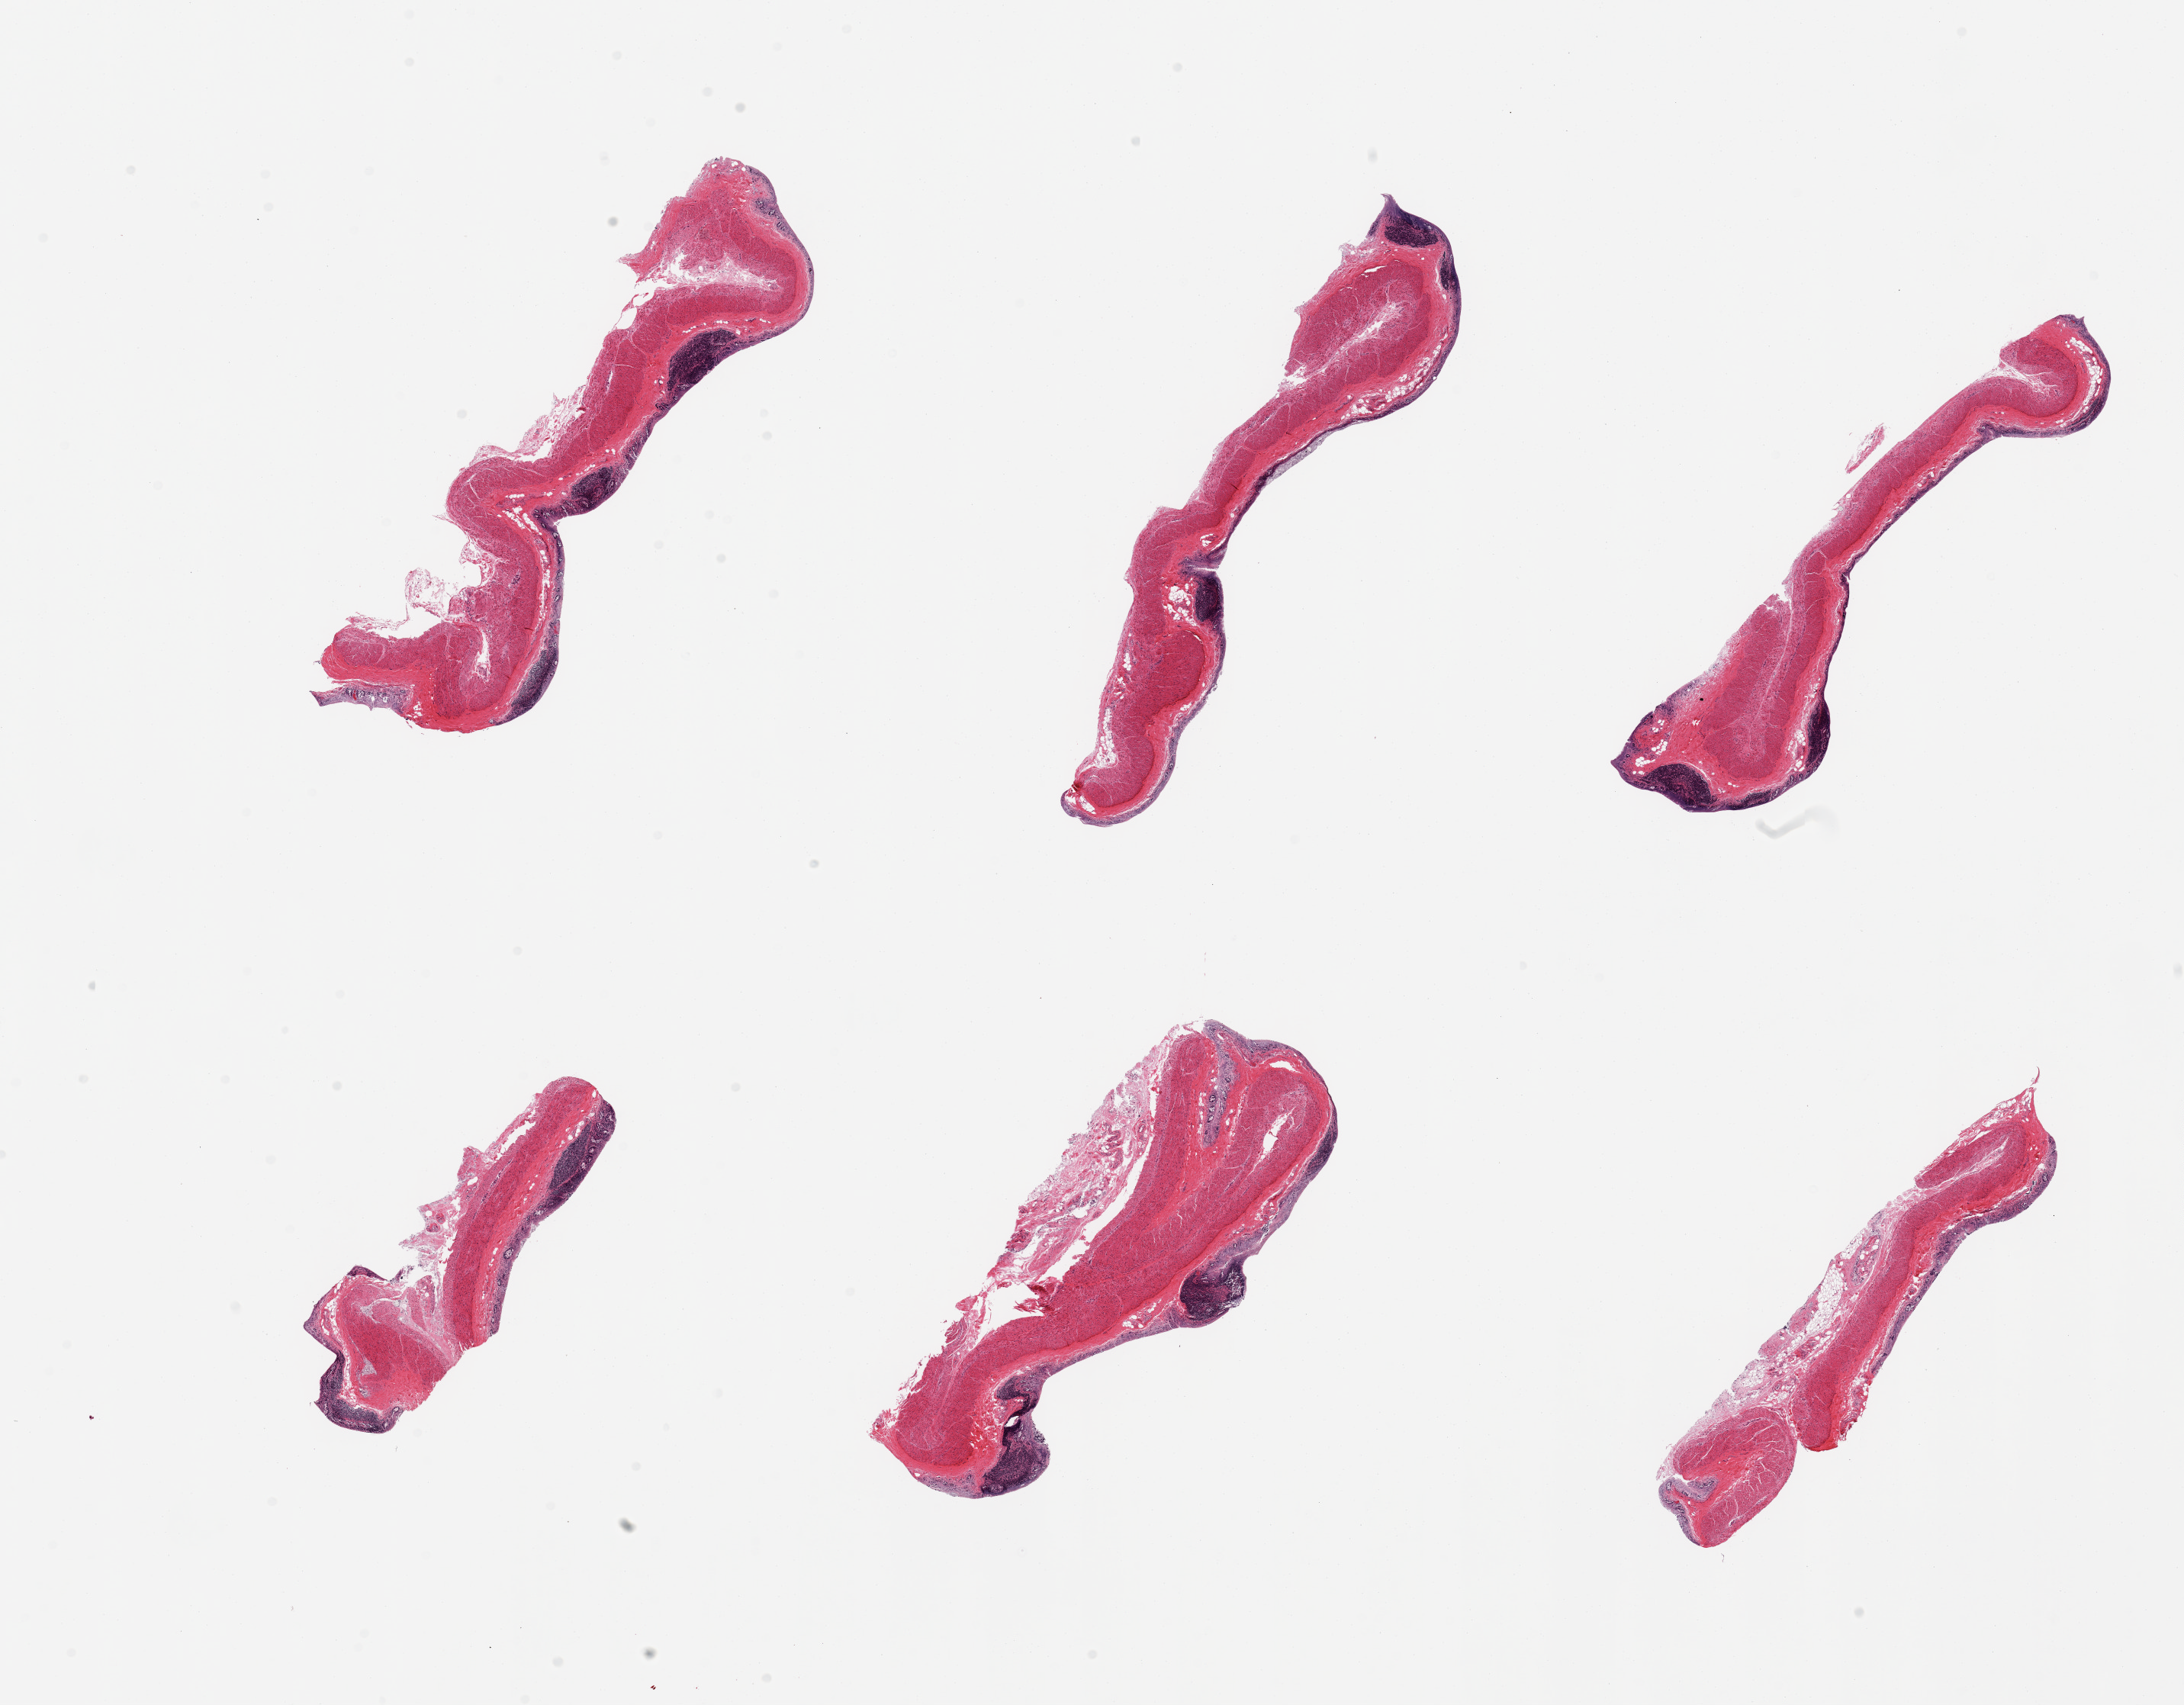
Whole-slide image, H&E stain — whole scanned area (about 22.6 x 17.7 mm, acquisition: 20x scan) shown as a low-resolution overview, PAXgene-fixed, paraffin-embedded tissue, section of transverse colon (target tissue), tissue donor sample. Donor: female.
Reviewer comment on this tissue sample: 6 pieces, mucosa autolyzed/sloughed.